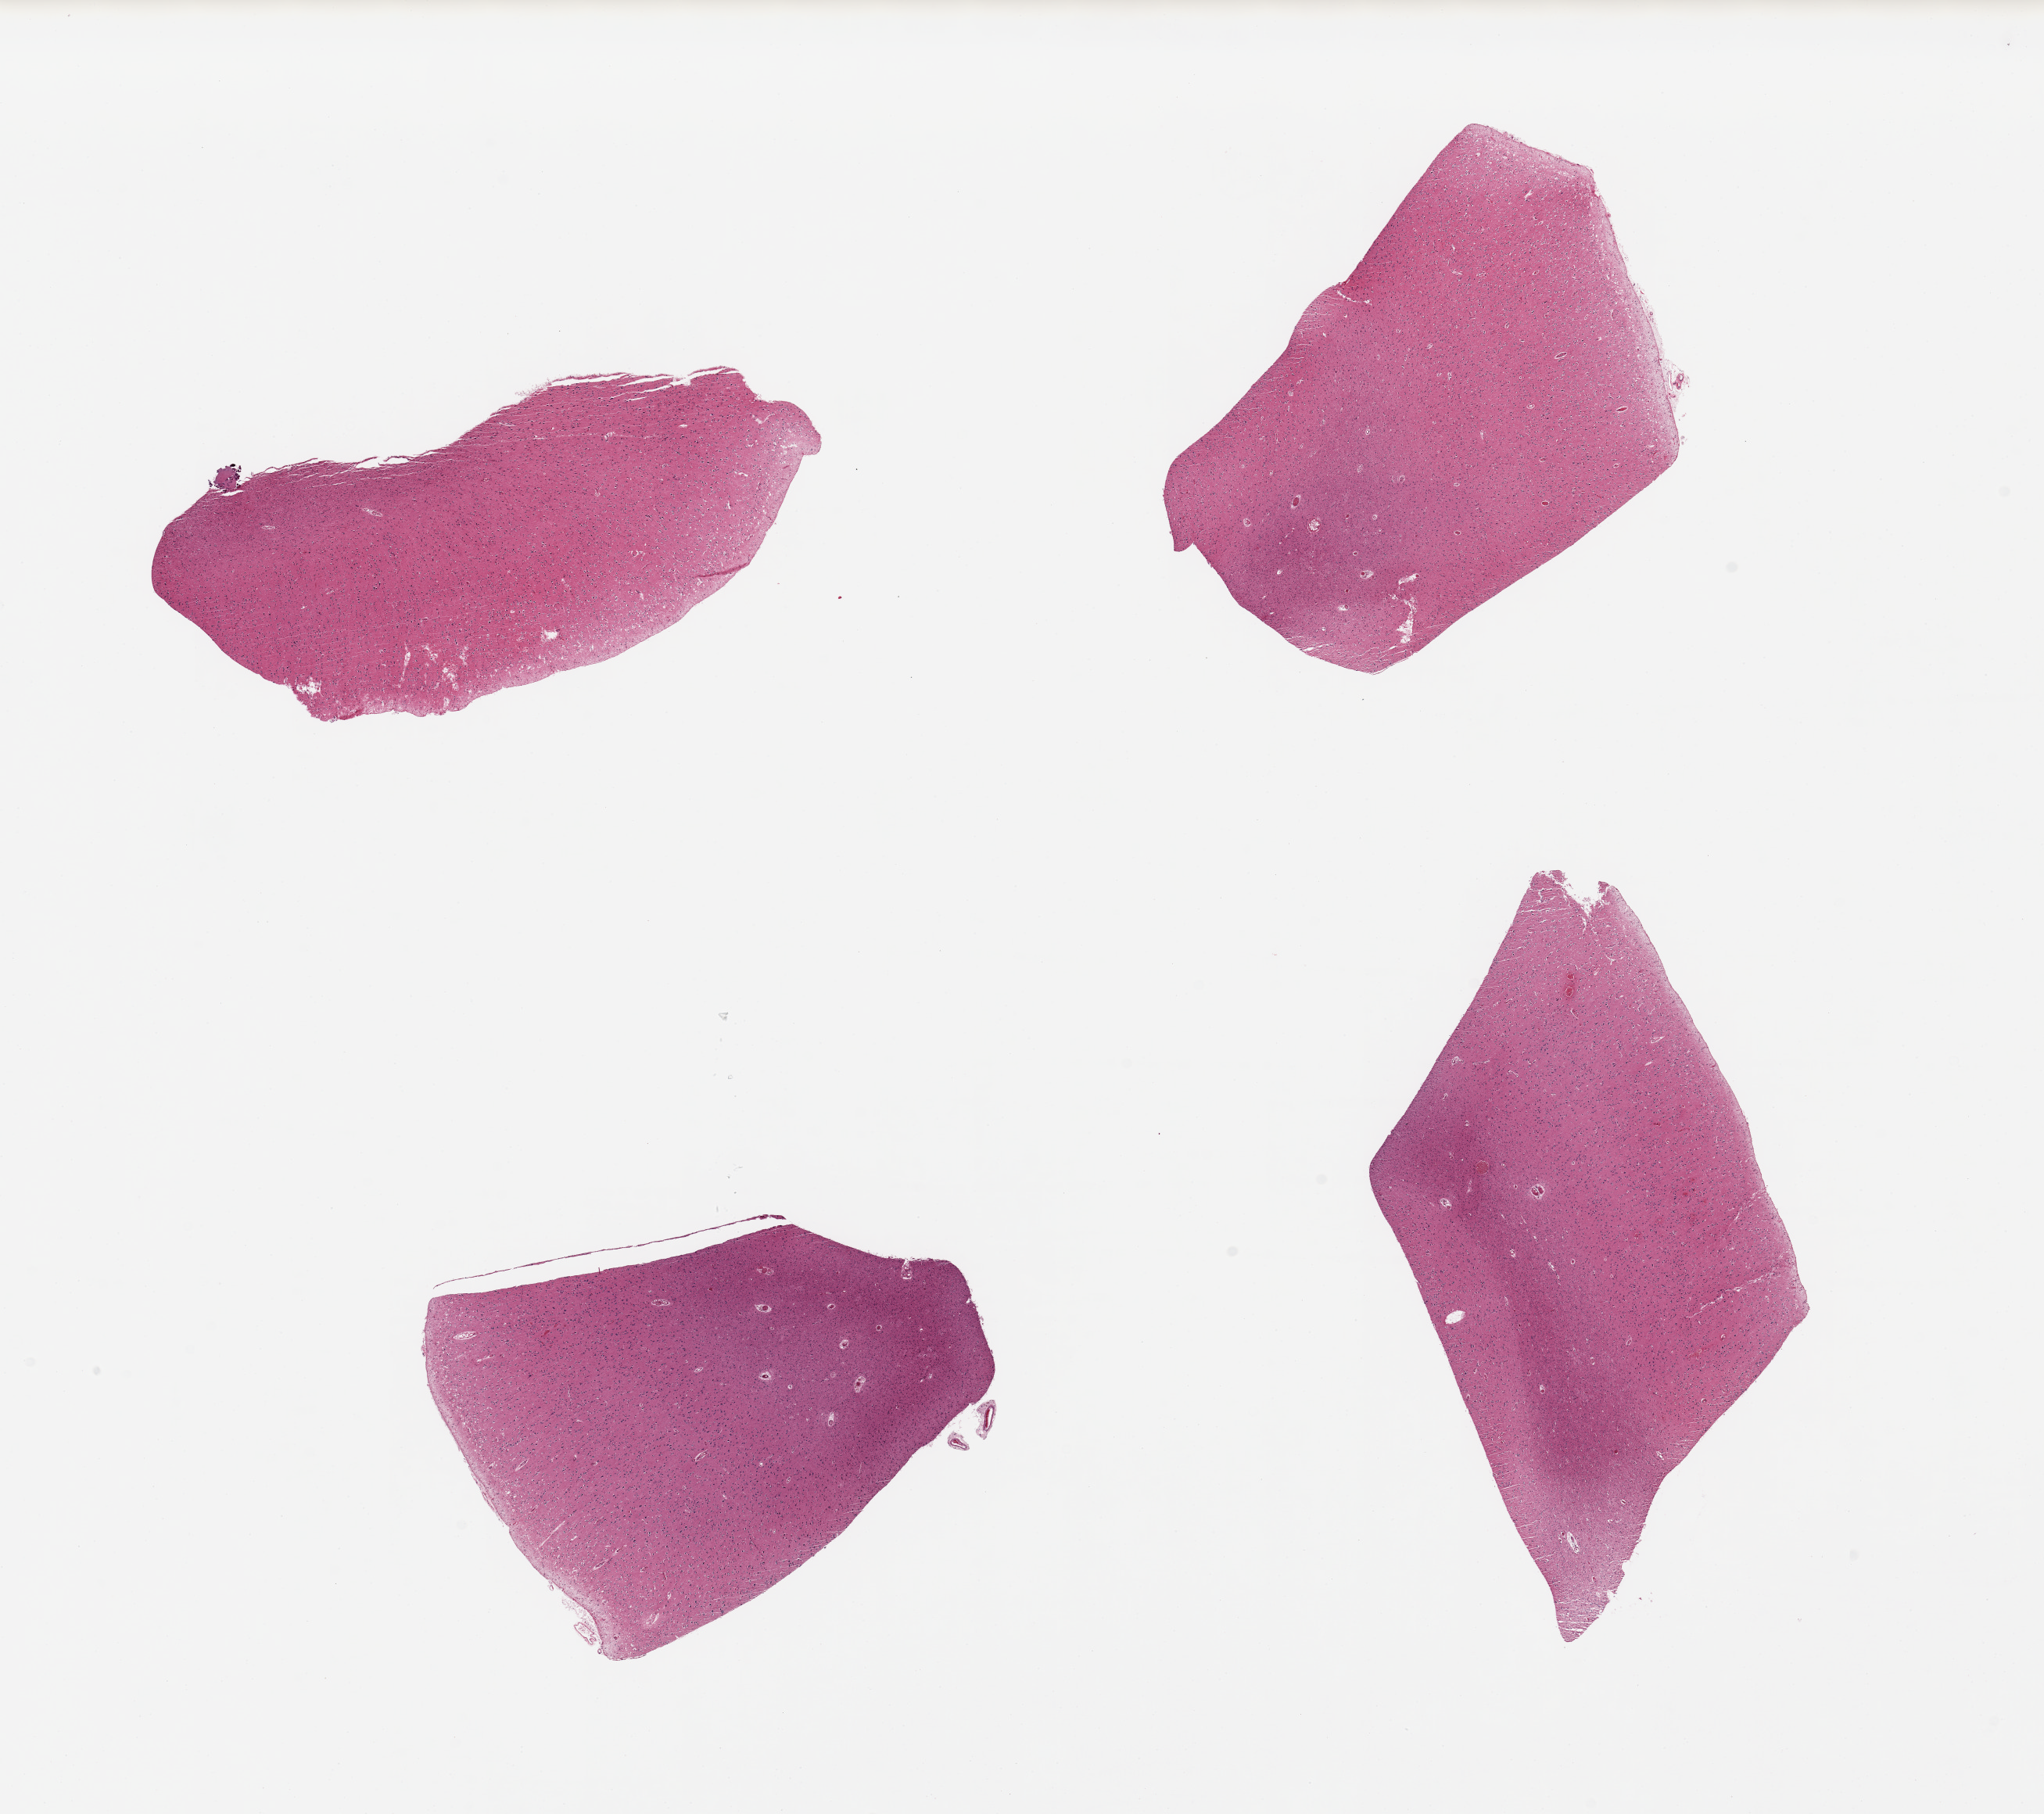
Digitized hematoxylin and eosin (H&E)-stained section, whole scanned area (about 20.7 x 18.3 mm) shown as a low-resolution overview. PAXgene-fixed paraffin-embedded (PFPE) section. Section of cerebral cortex (target tissue). Donor tissue sample. Male donor.
Pathologist's review note for this sample: 4 pieces.